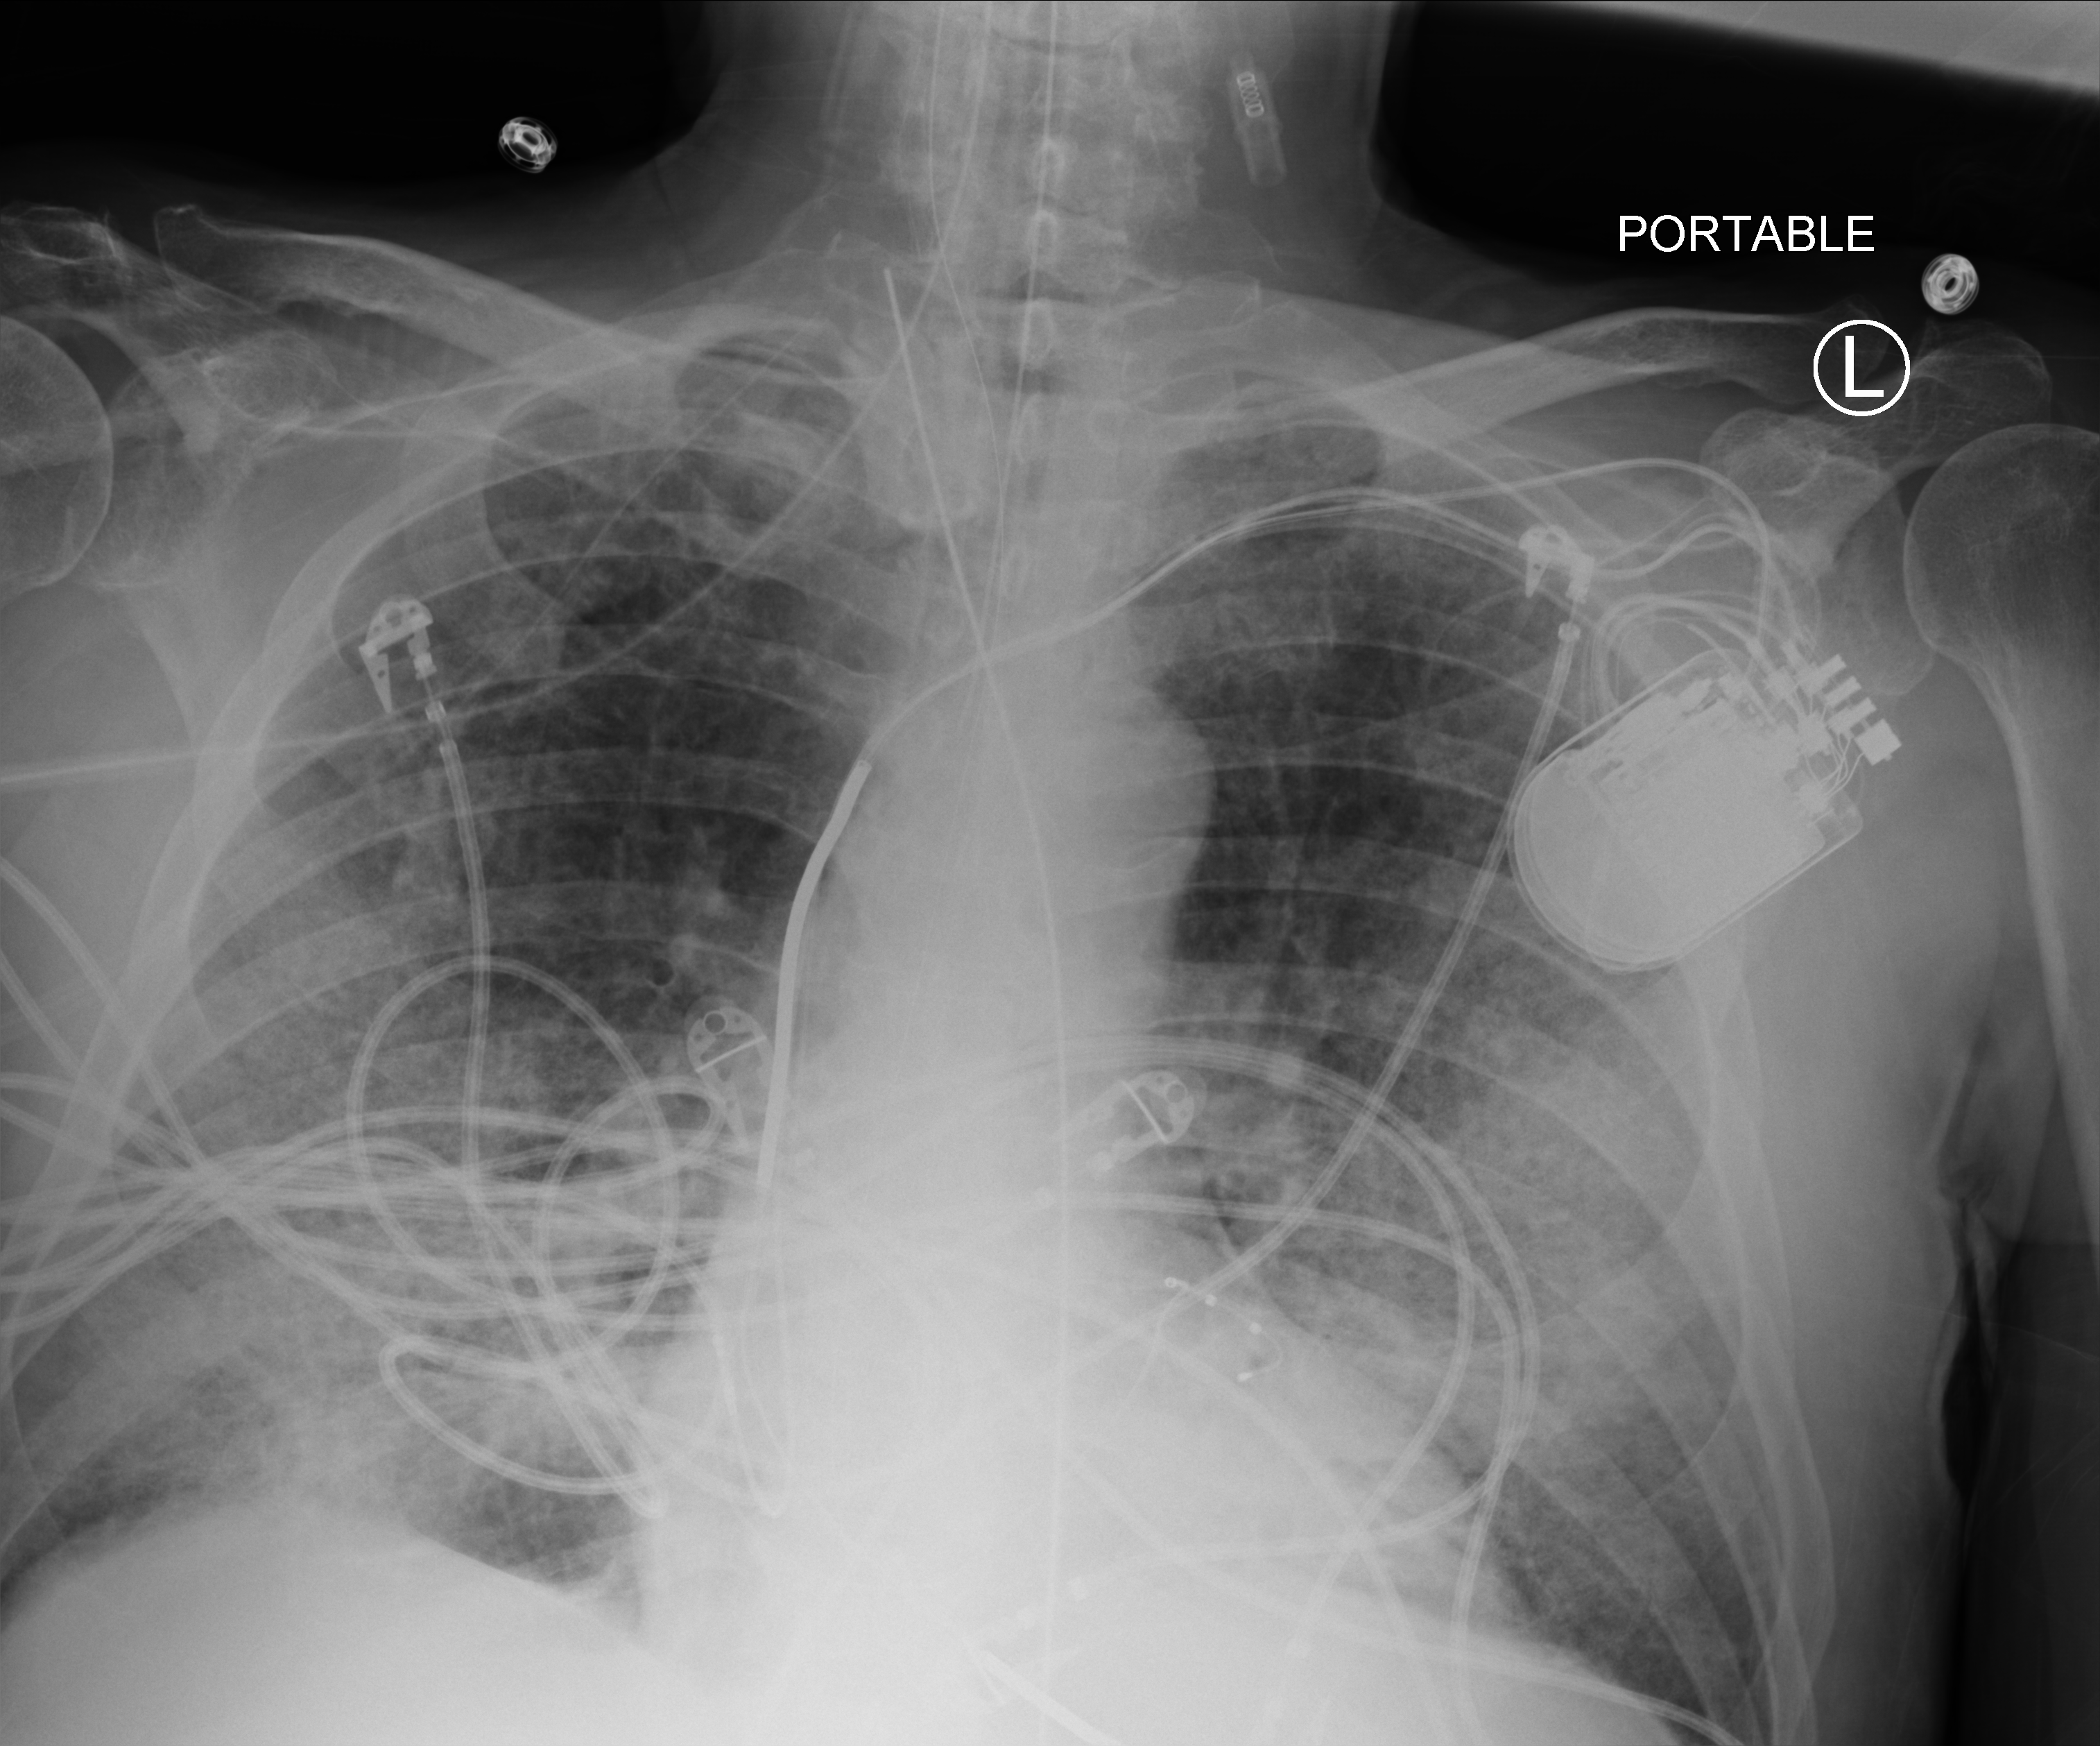
Bedside chest radiograph (computed radiography), anteroposterior (AP) projection. Patient hospitalised with COVID-19; male, aged 60–74 years.
Admission-level facts for this patient (not findings on this image; timing relative to this image not recorded):
- mechanically ventilated during this hospital stay: yes
- admitted to intensive care during this hospital stay: yes